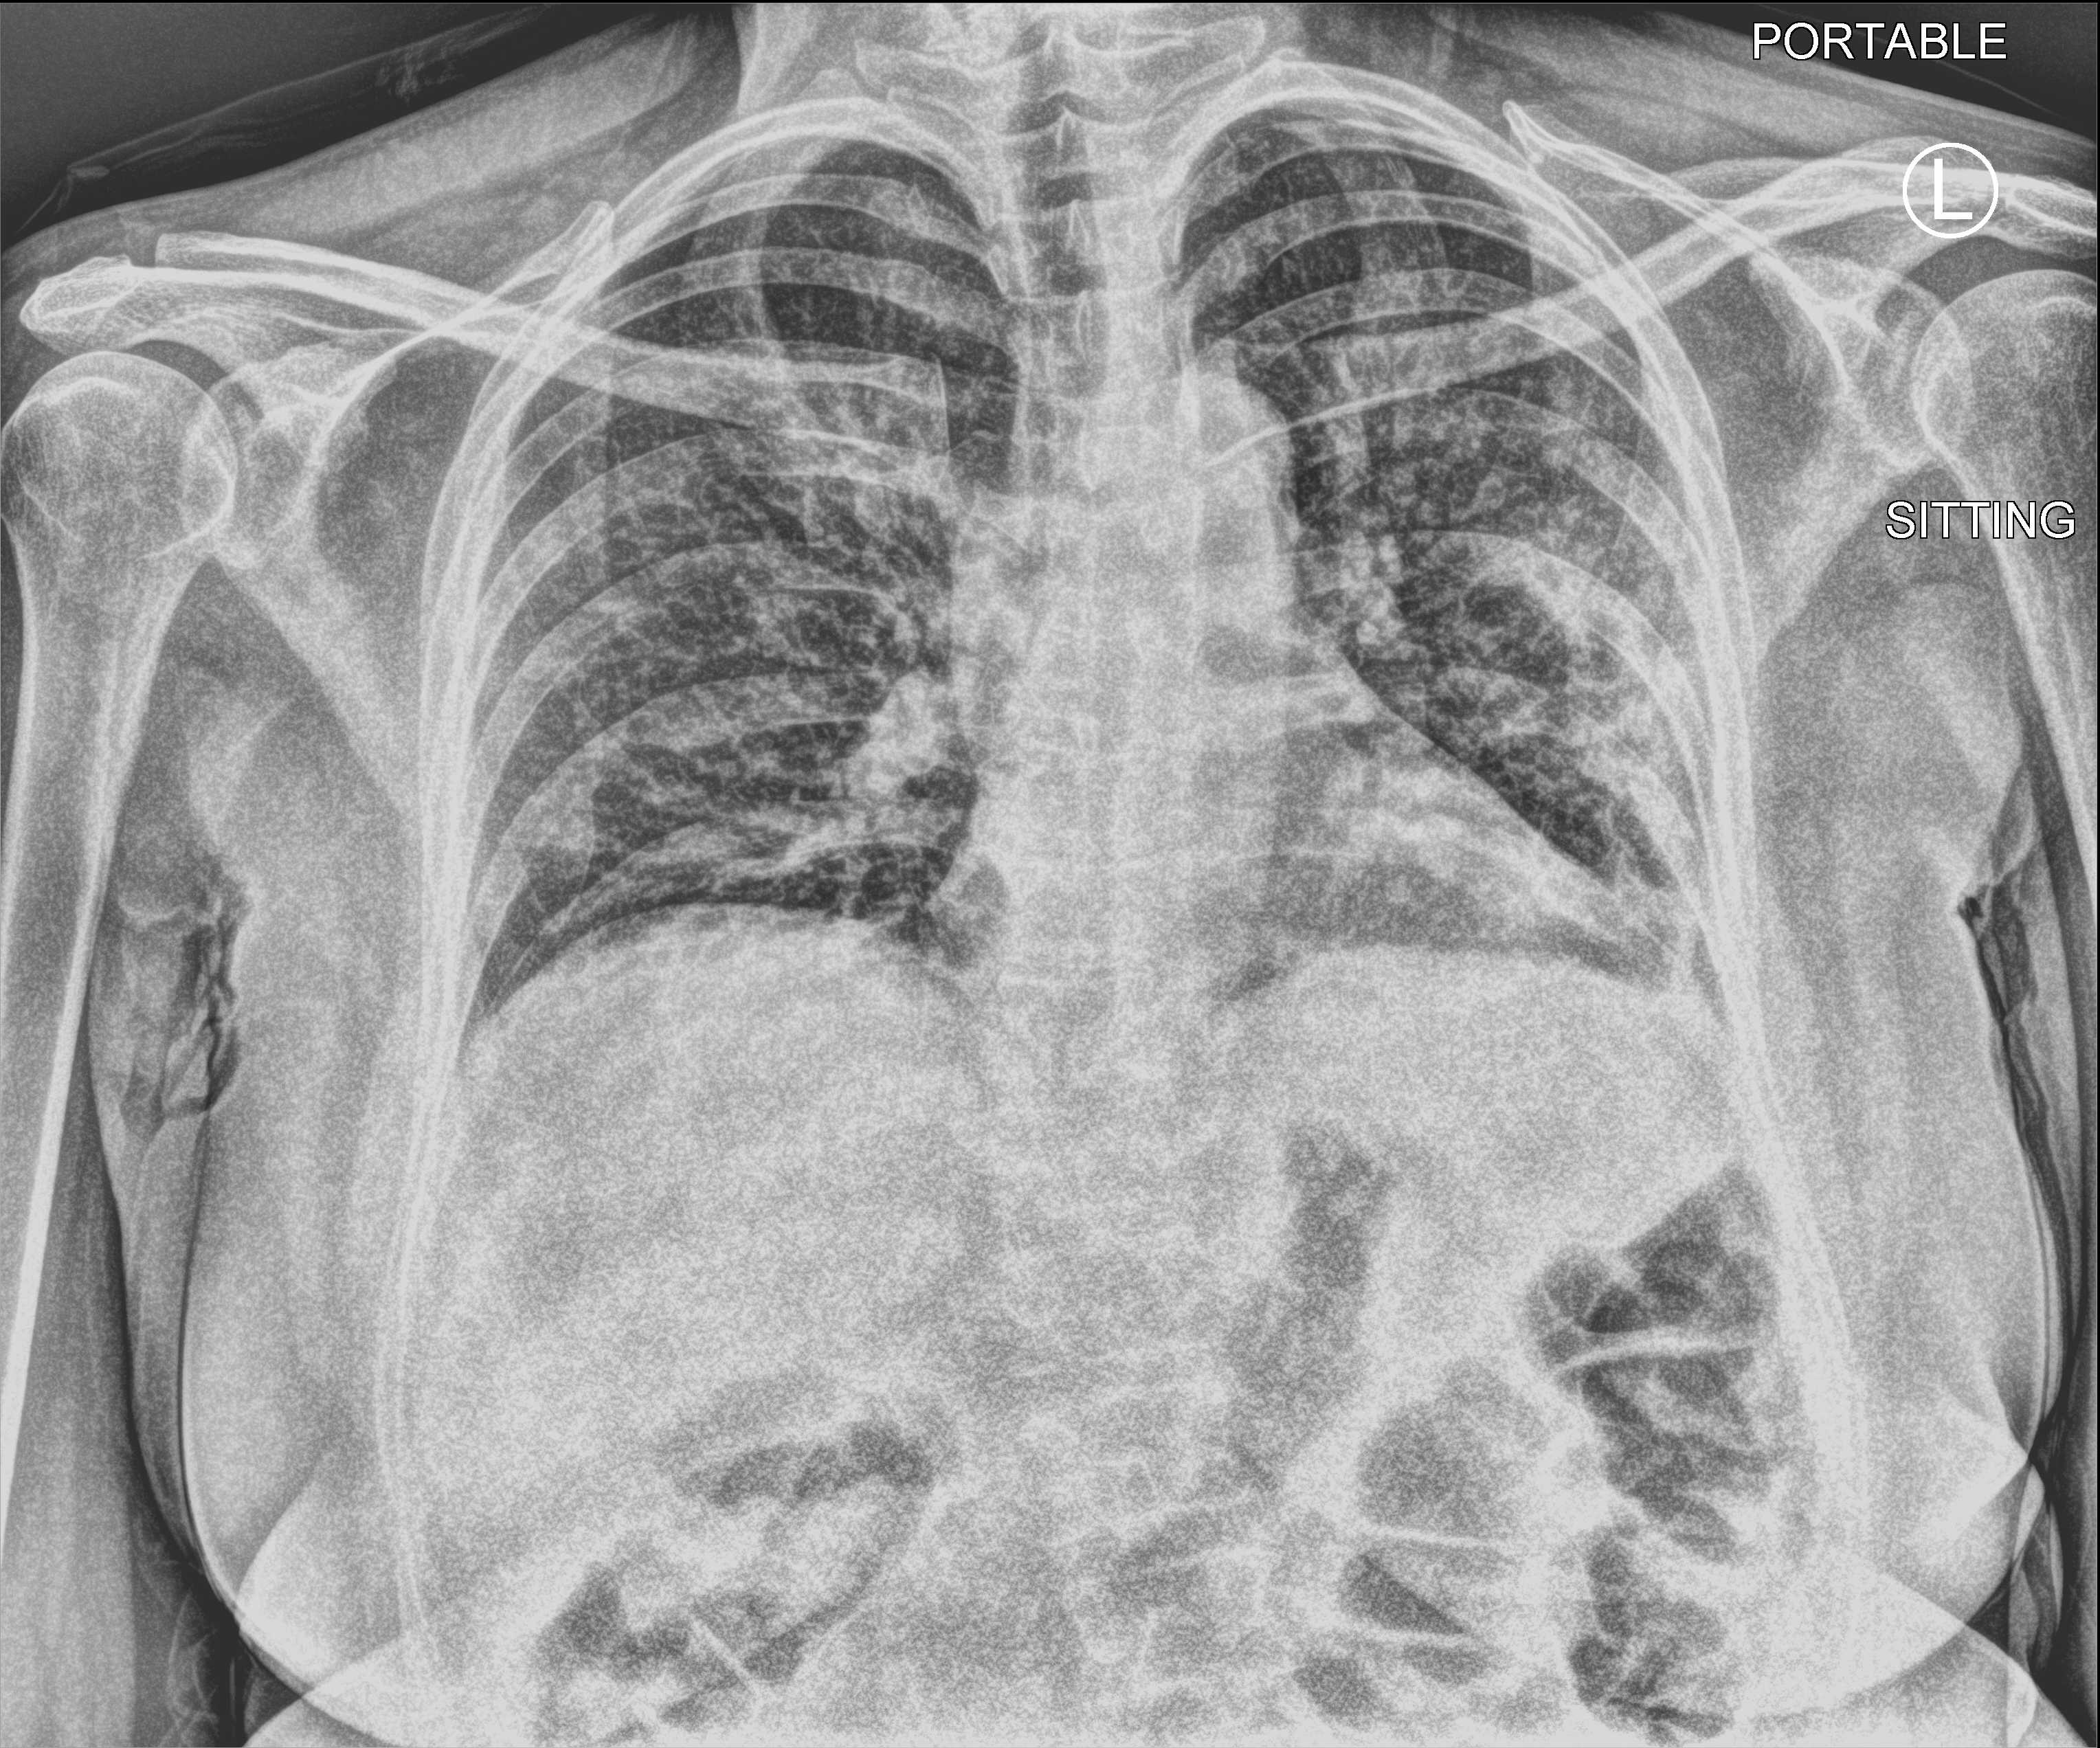
Bedside chest radiograph (computed radiography); anteroposterior (AP) projection. Patient hospitalised with COVID-19; female, aged 18–59 years.
Hospital-stay facts (about this admission, not read from this image; timing relative to this image not recorded): mechanically ventilated during this hospital stay: no.